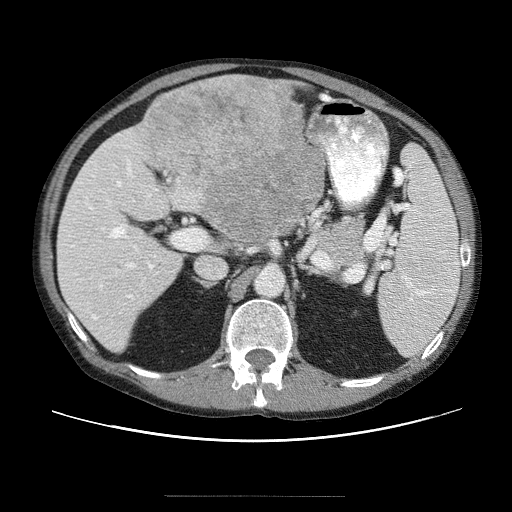
Contrast-enhanced abdominal CT (liver protocol), one axial slice. Position 23 of 69 along the scan axis. Reconstruction kernel STANDARD. 120 kVp. Soft-tissue window (W 400 / L 40 HU). 2.5 mm slice thickness. 512 × 512 image matrix, field of view 380 × 380 mm. From the clinical record (not read from this slice): diagnosis: hepatocellular carcinoma (patient treated with transarterial chemoembolisation; whether this scan precedes or follows treatment is not stated here); TNM stage (as recorded): Stage-IVB.
Annotated regions visible in this slice (semi-automatically segmented with operator editing):
- liver parenchyma outside the tumour (the mass and vessels are separate outlines, so this box may not span the whole liver): bounding box (x1, y1, x2, y2) in pixels: (56, 80, 322, 348)
- mass: (133, 77, 328, 248)
- liver vessels: (65, 157, 170, 326)